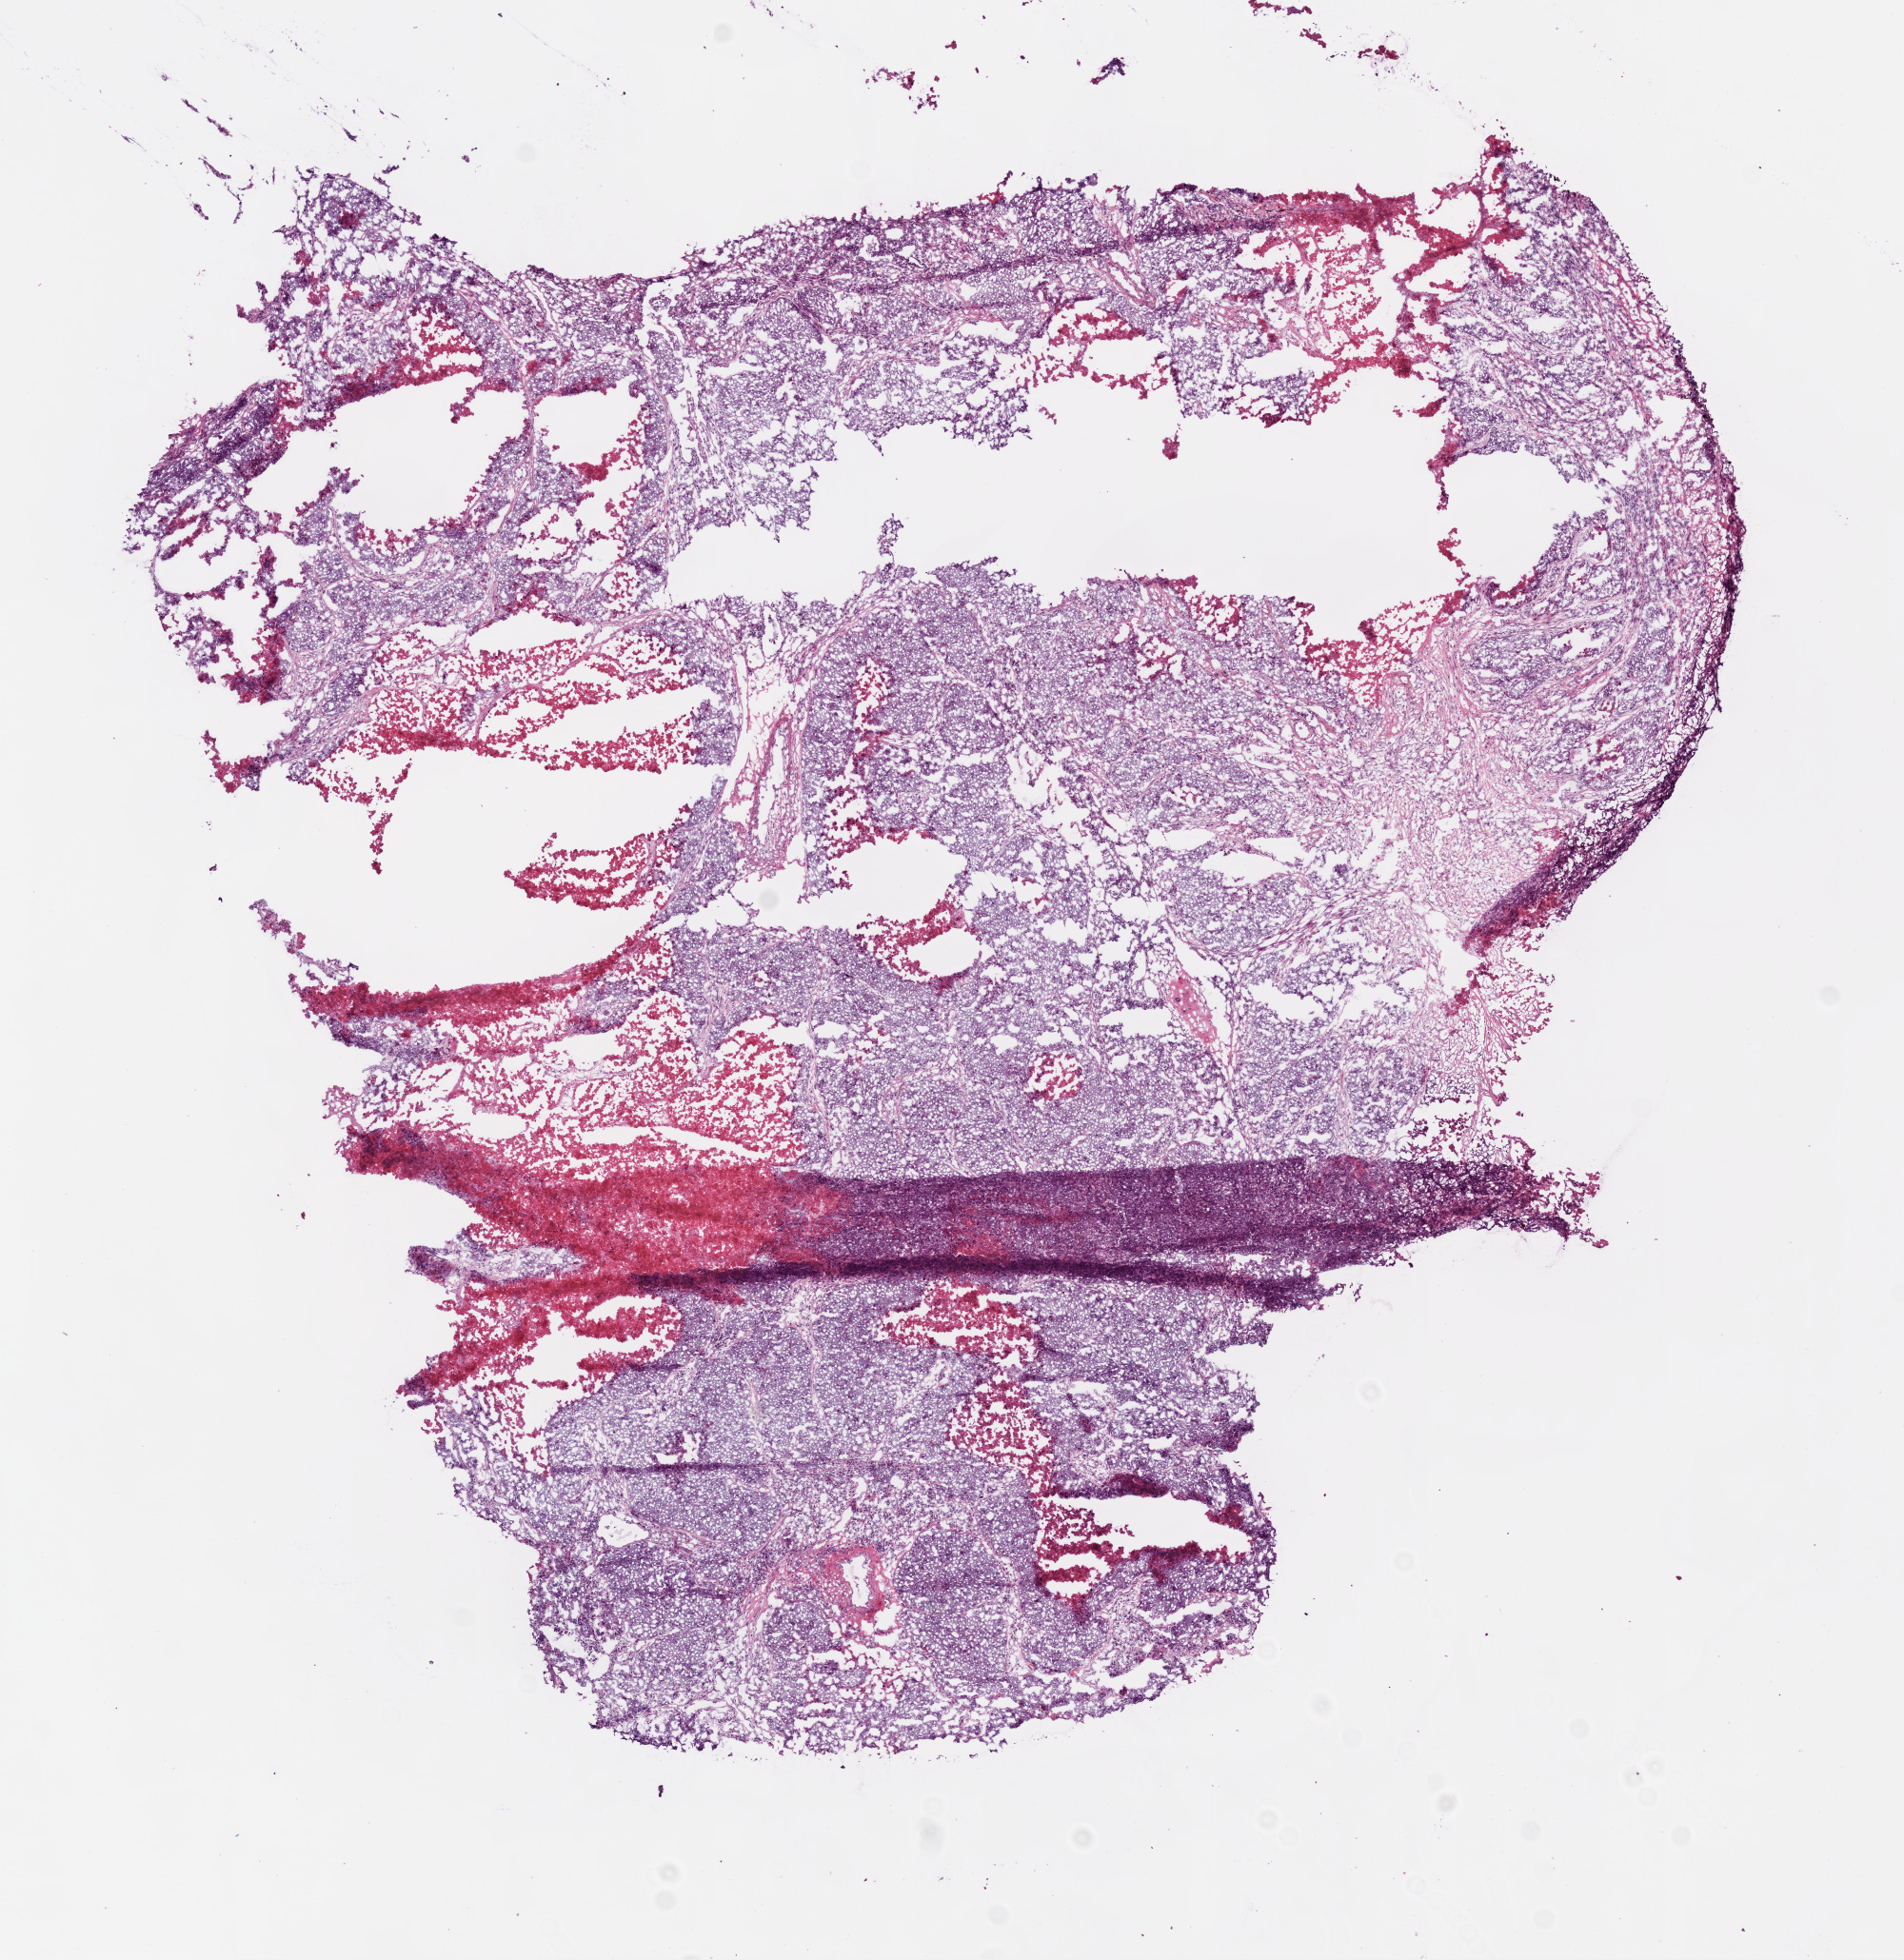
Digitized Hematoxylin and eosin (H&E) stained tissue section (whole slide), low-resolution overview of the scanned area, about 8.0 x 8.3 mm (from a 20x scan), frozen section from the bottom of the tissue portion, sample: primary tumour, lung. Female, age 59 years at initial diagnosis. Pathologist review of this section (percent, as recorded): tumour cells 80%, tumour nuclei 90%, normal cells 0%, stromal cells 5%, necrosis 15%.
- TNM: T1 N0 M0
- laterality: left
- pathologic diagnosis: Squamous cell carcinoma, NOS (upper lobe, lung)
- AJCC pathologic stage: IA (6th edition)